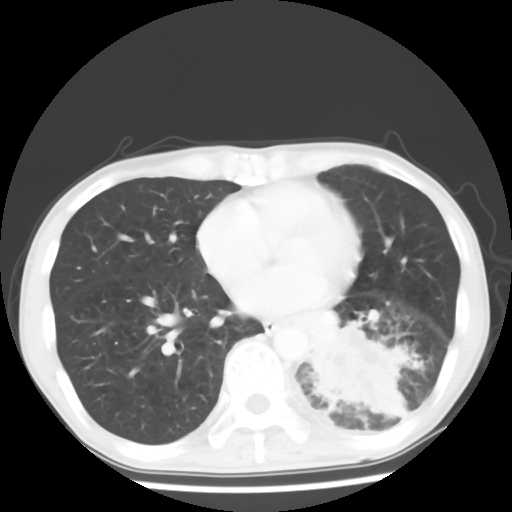
Chest CT, one axial slice. Slice 24 of 64 in the series (ordered by position). Reconstruction kernel STANDARD. 120 kVp. Lung window (W 1500 / L -600 HU). 5 mm slice thickness. 512 × 512 image matrix. Male patient, age 68 years. From the clinical record (not read from this slice): clinical TNM (as recorded): T4 N0 M0.
Annotated regions visible in this slice (rectangle marked by the reading radiologist):
- lung tumour (recorded histology: squamous cell carcinoma): bounding box (x1, y1, x2, y2) in pixels: (289, 301, 417, 451)